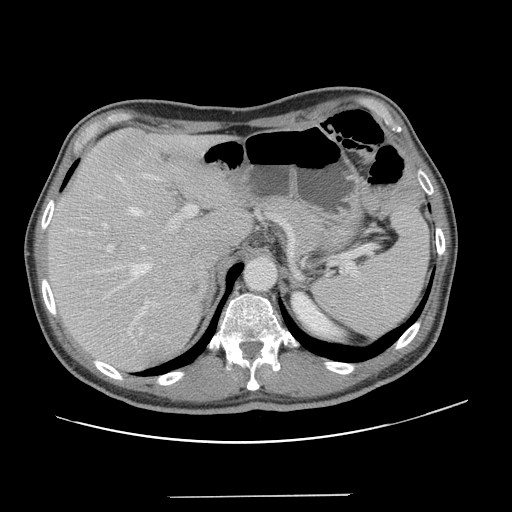
Contrast-enhanced abdominal CT, one axial slice. Slice 93 of 131 in the series (ordered by position). 120 kVp. Soft-tissue window (W 400 / L 40 HU). 512 × 512 image matrix. Male patient, age 60 years. Case-level facts recorded for this patient, not image findings: diagnosis: colorectal cancer liver metastases, imaged before liver resection; multiple liver metastases: no; largest metastasis: 2.5 cm; chemotherapy before resection: no.
Annotated regions visible in this slice (outlined manually by an expert reader):
- hepatic veins: box from (x=94, y=174) to (x=152, y=299) px
- liver: (x=47, y=129)–(x=249, y=371)
- planned liver remnant (the part of the liver to remain after resection): (x=47, y=129)–(x=249, y=354)
- portal vein (with intrahepatic branches): (x=101, y=144)–(x=198, y=330)
- liver metastasis: (x=188, y=283)–(x=202, y=296)